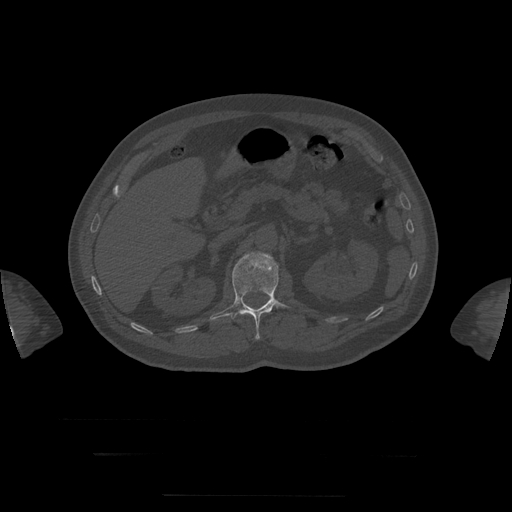
CT including the spine, one axial slice; reconstruction kernel STANDARD; bone window (W 1800 / L 400 HU); 512 × 512 image matrix, field of view 510 × 510 mm. Patient age 73 years. Case-level facts recorded for this patient, not image findings: primary cancer: prostate.
Structures marked on this image (semi-automatically segmented with operator editing):
- L1 vertebra: bounding box (x1, y1, x2, y2) in pixels: (210, 253, 290, 340)